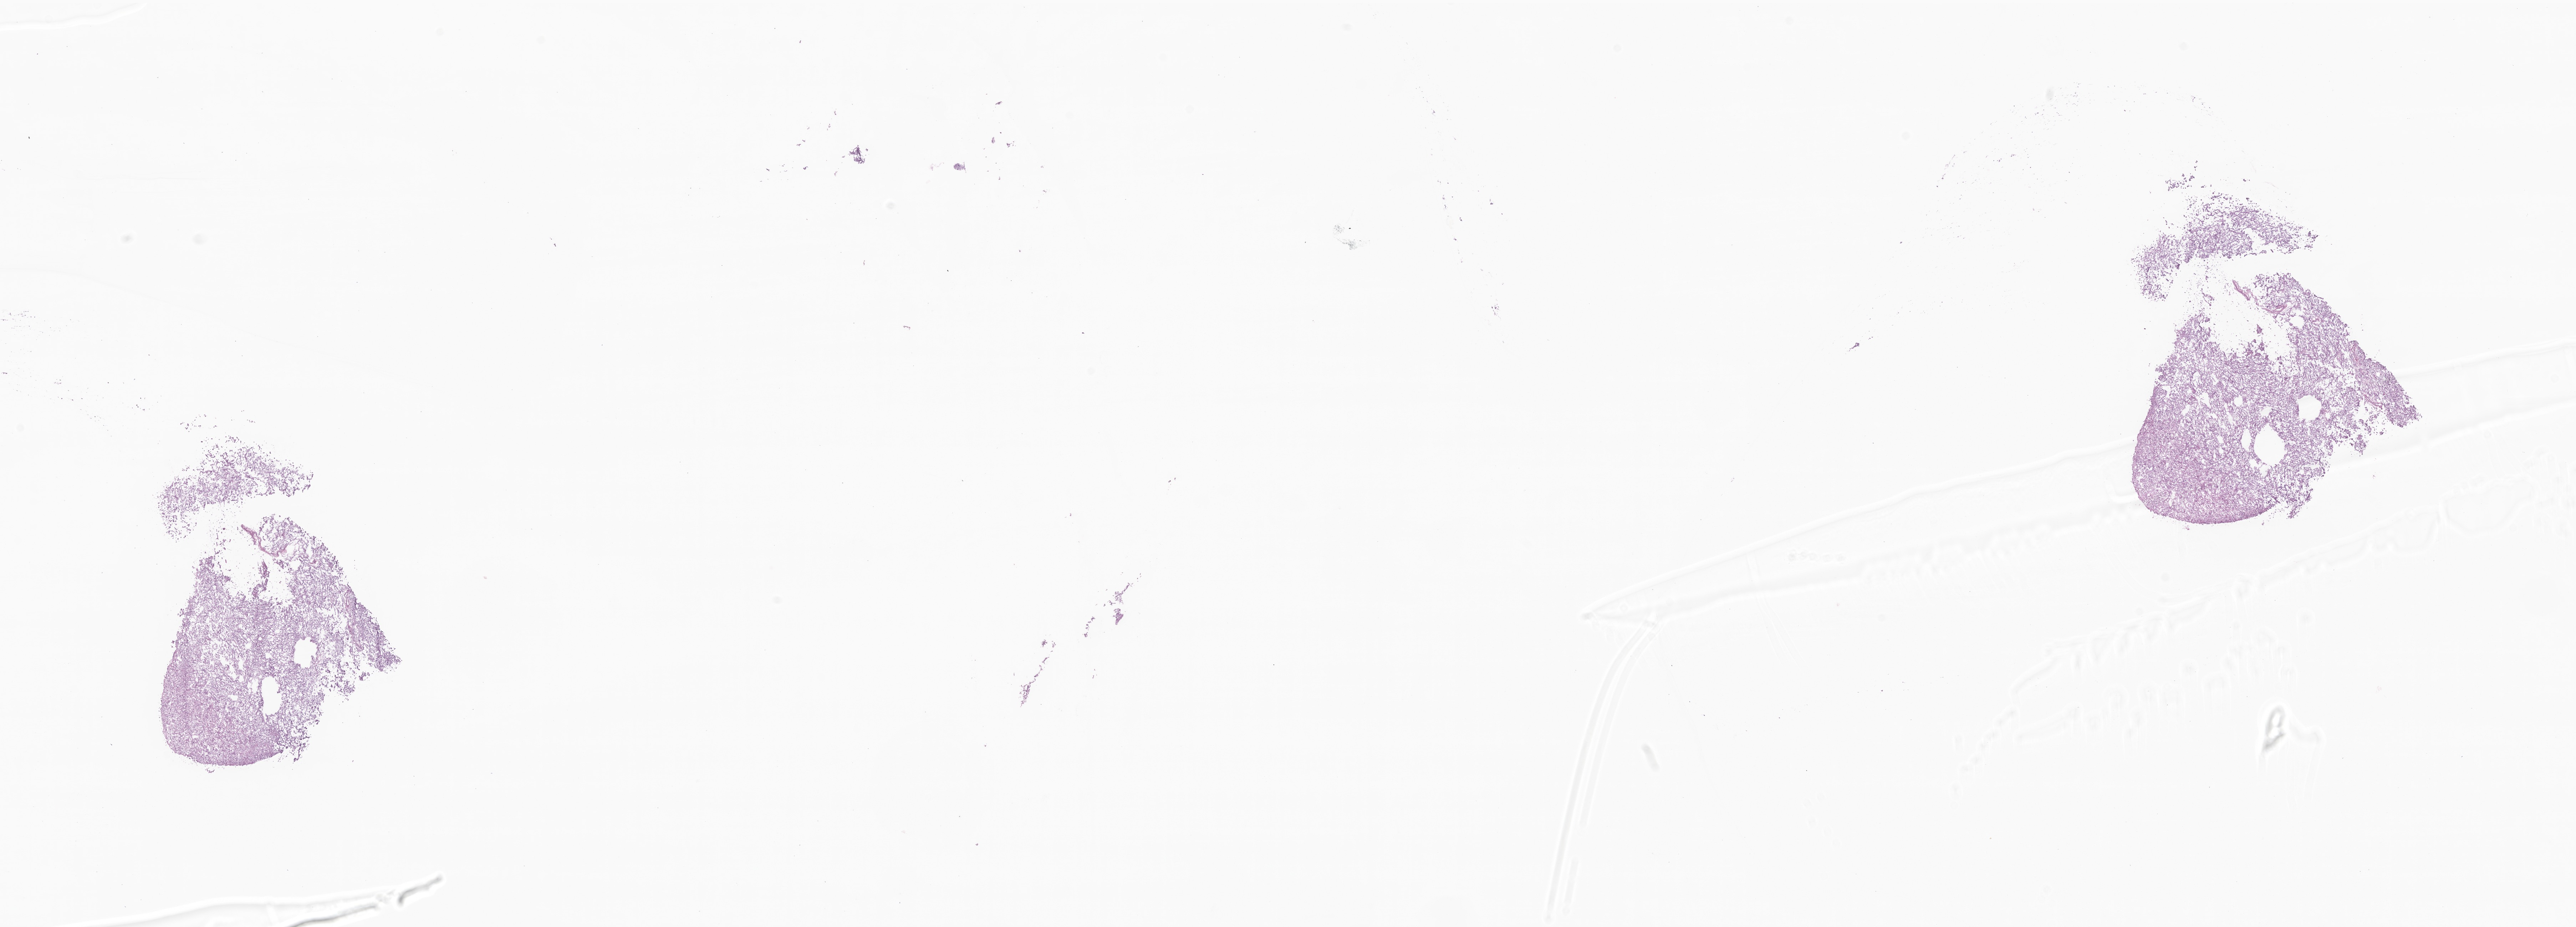
Whole-slide image, haematoxylin and eosin stain of tumor tissue from the parietal lobe — whole scanned area (about 30.5 x 11.0 mm) shown as a low-resolution overview. Cryosection (OCT / tissue freezing medium). Female patient, age 205 months (17 years 1 month).
* diagnosis: Pleomorphic xanthoastrocytoma, NOS